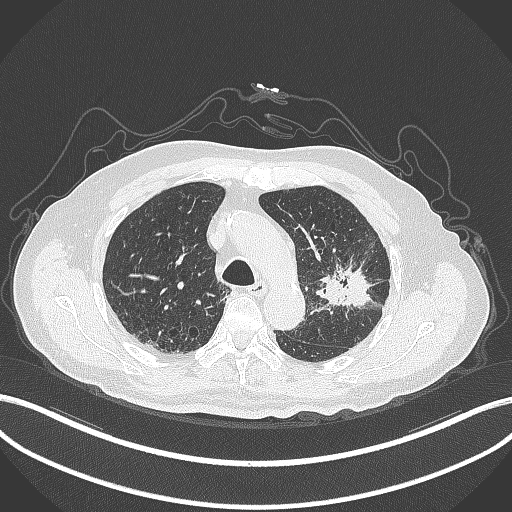
Chest CT, one axial slice. Position 213 of 331 along the scan axis. Lung window (W 1500 / L -600 HU). 512 × 512 image matrix. Patient: male, 79 years. Case-level facts recorded for this patient, not image findings: clinical TNM (as recorded): T2a N1 M1; histopathological grade: G3.
Annotated regions visible in this slice (bounding box drawn by a radiologist):
- lung tumour (recorded histology: adenocarcinoma): bounding box [x1, y1, x2, y2] px = [316, 255, 386, 314]